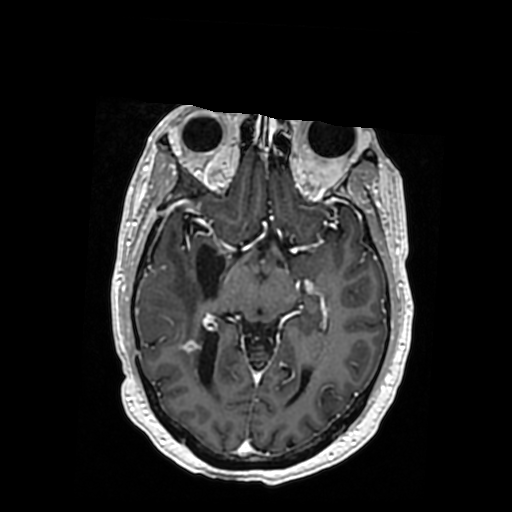
Brain MRI from a brain-tumour surgery series, one axial slice; slice 203 of 364 in the series (ordered by position); T1-weighted post-contrast; 512 × 512 image matrix, field of view 260 × 260 mm. Case-level facts recorded for this patient, not image findings: histopathology: Oligodendroglioma; WHO grade: 3; IDH mutation: yes; tumour location: Right Posterior Temporal Inferior Parietal.
Annotated regions visible in this slice (manually delineated by an expert):
- previous resection cavity: box from (x=196, y=243) to (x=225, y=297) px
- tumour: (x=149, y=336)–(x=164, y=347)